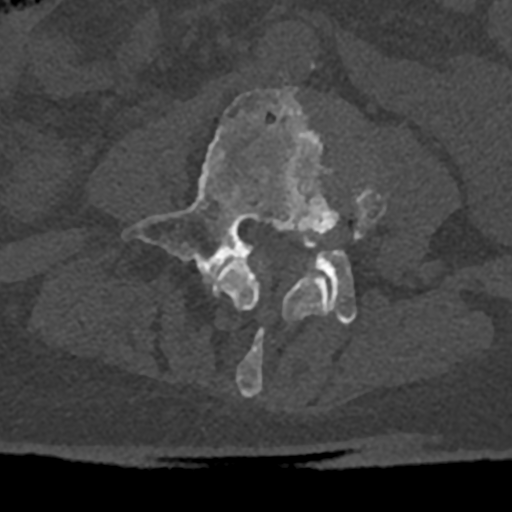
CT including the spine, one axial slice; position 281 of 797 along the scan axis; reconstruction kernel Br40s/3; bone window (W 1800 / L 400 HU); 0.5 mm slice thickness; 512 × 512 image matrix, field of view 160 × 160 mm. Male patient, age 74 years. From the clinical record (not read from this slice): primary cancer: renal; vertebrae with lytic lesions (as recorded): T10, L1, L2, L3, L4, L5.
Annotated regions visible in this slice (semi-automatically segmented with operator editing):
- L3 vertebra: bounding box (x1, y1, x2, y2) in pixels: (213, 176, 386, 397)
- L4 vertebra: (124, 88, 356, 325)